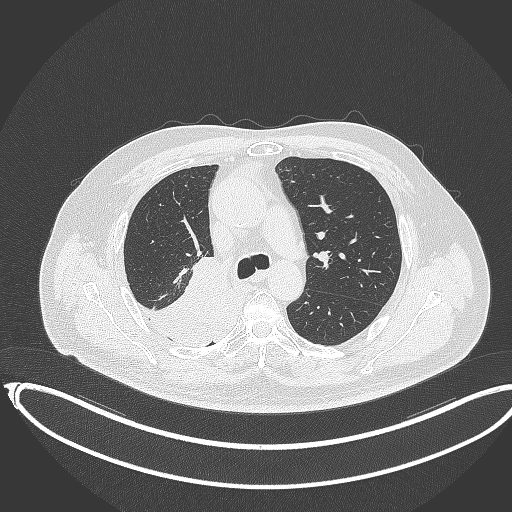
Chest CT, one axial slice; reconstruction kernel B70f; lung window (W 1500 / L -600 HU); 1 mm slice thickness; 512 × 512 image matrix. Patient: male, 68 years. From the clinical record (not read from this slice): clinical TNM (as recorded): T2a N0 M0.
Outlined on this slice (bounding box drawn by a radiologist):
- lung tumour (recorded histology: adenocarcinoma): bounding box (x1, y1, x2, y2) in pixels: (128, 253, 242, 350)